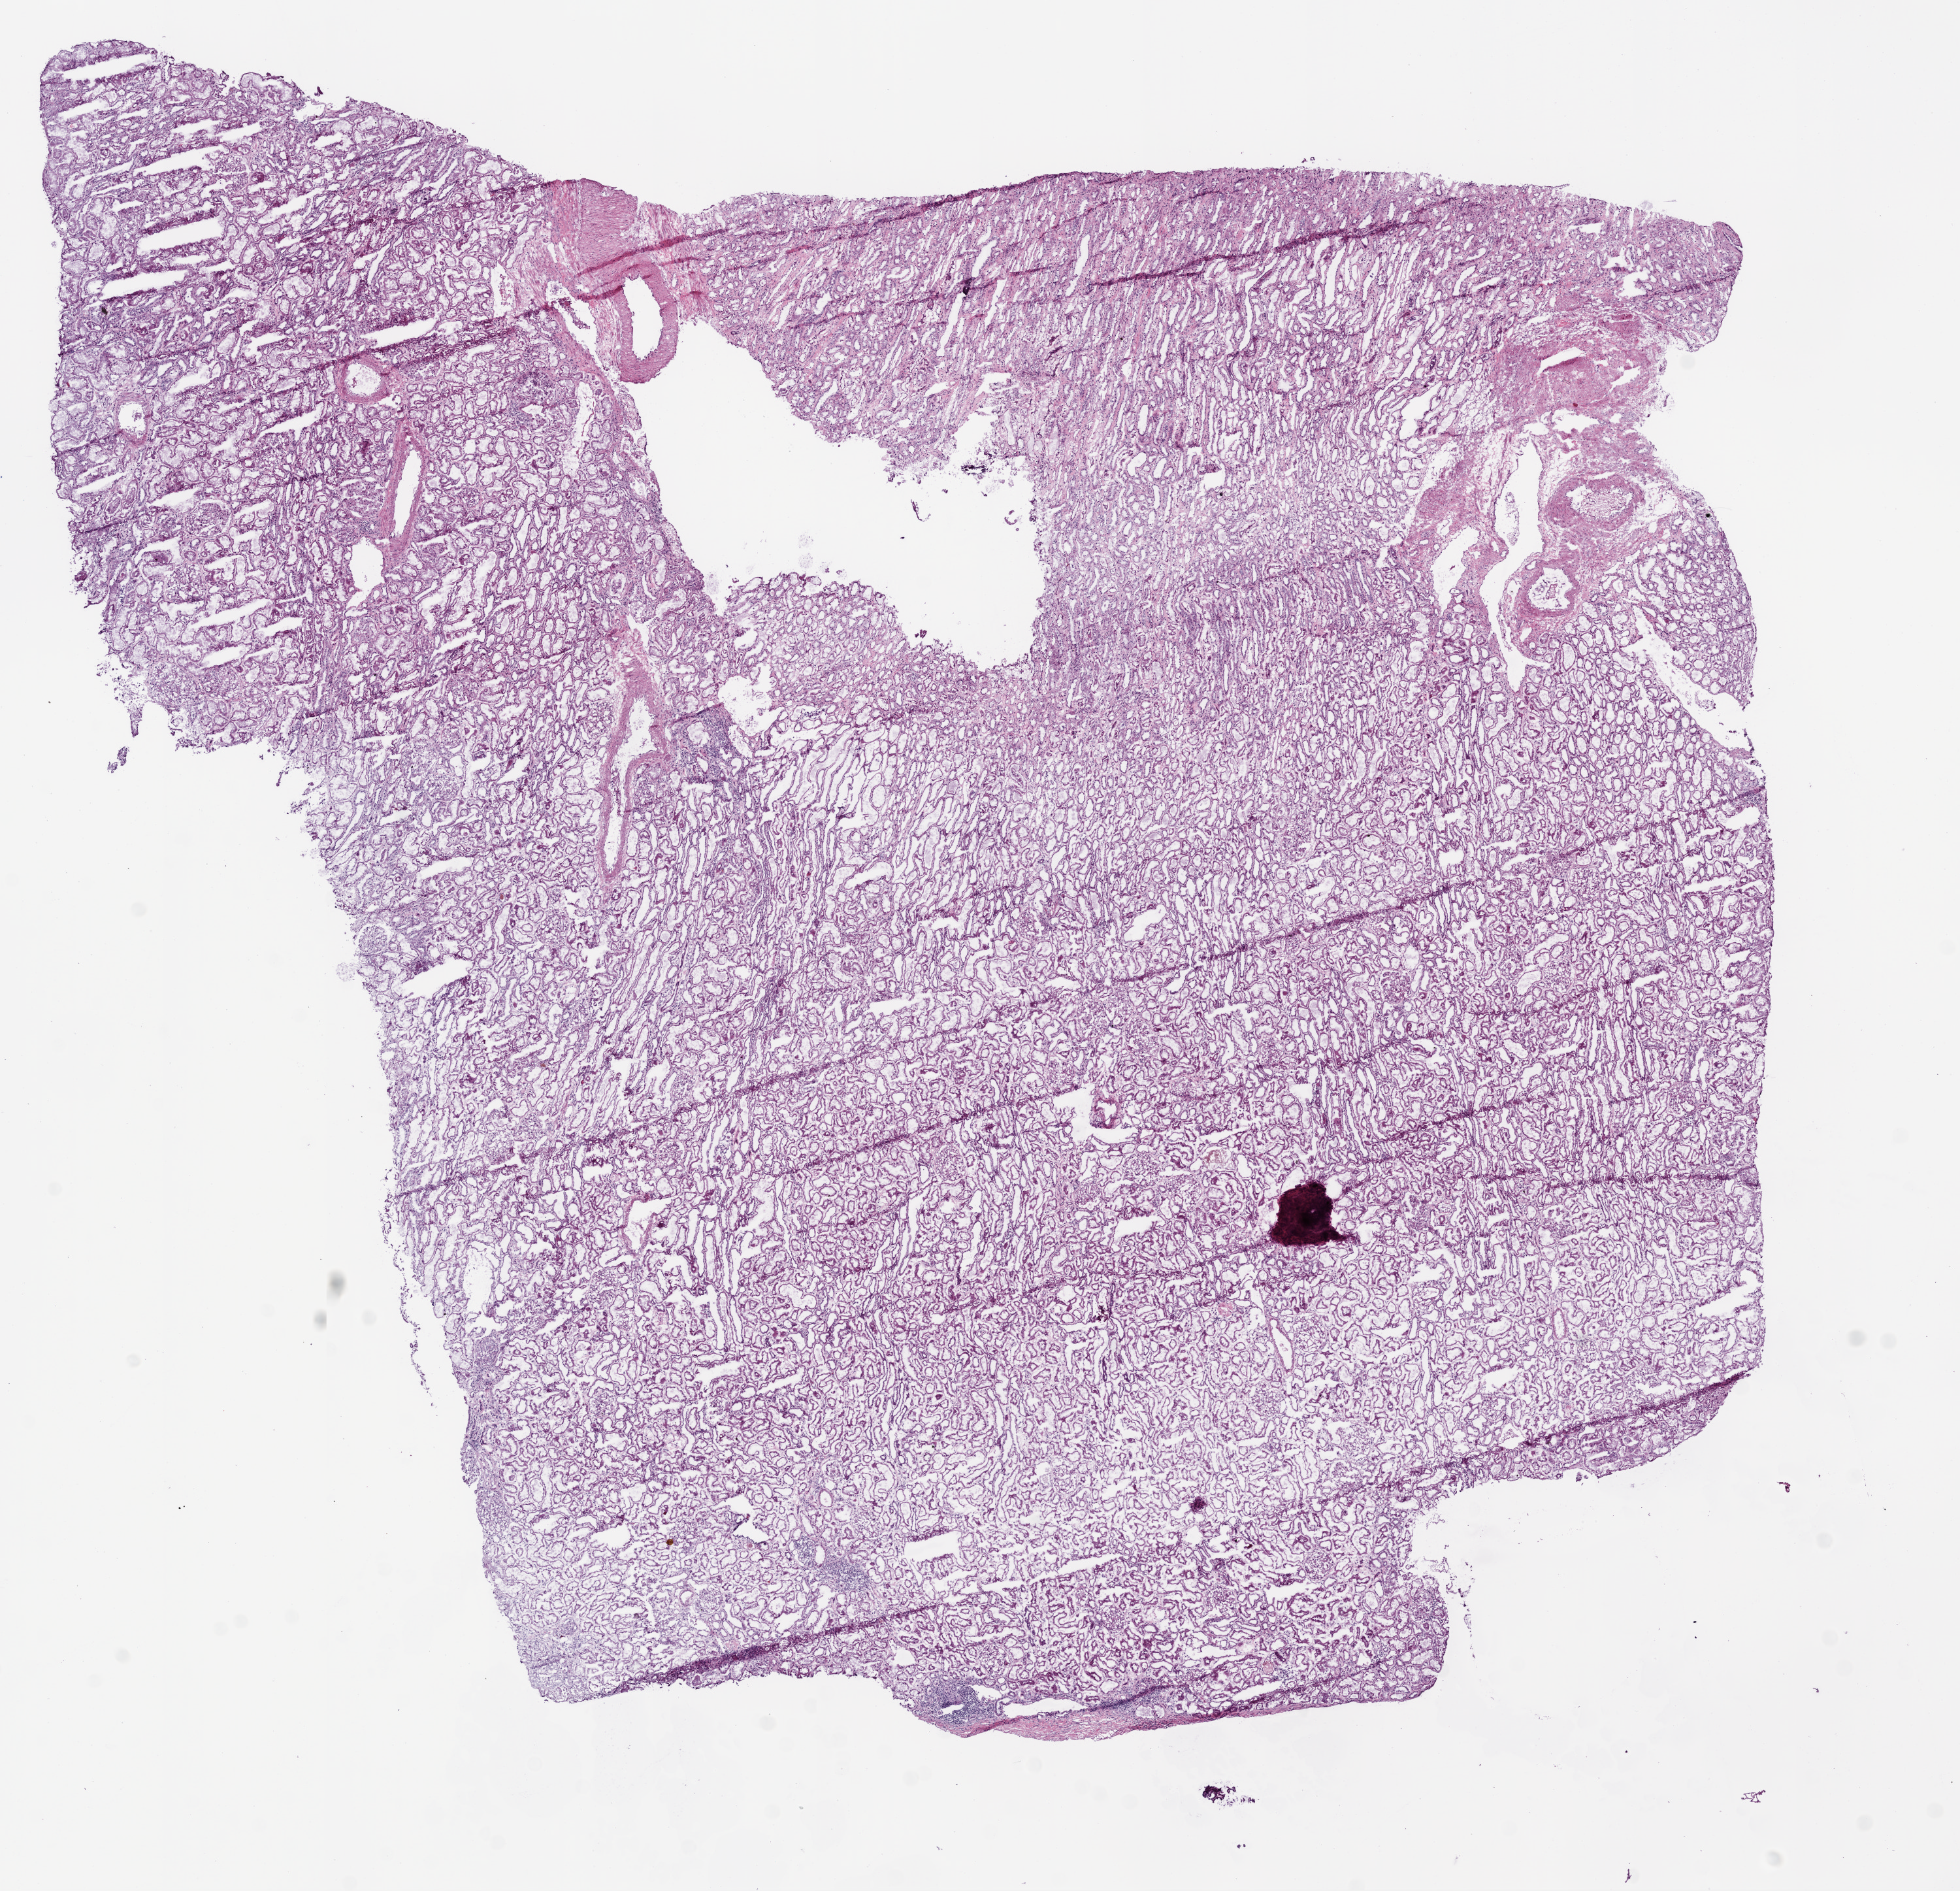
Digitized Hematoxylin and eosin (H&E) stained tissue section (whole slide) — low-resolution overview of the scanned area, about 12.0 x 11.6 mm, frozen section from the bottom of the tissue portion, sample: solid tissue normal (non-tumour tissue), kidney. Male, age 40 years at initial diagnosis.
This section: solid tissue normal (non-tumour) sample from the same patient. Patient diagnosis: Clear cell adenocarcinoma, NOS.